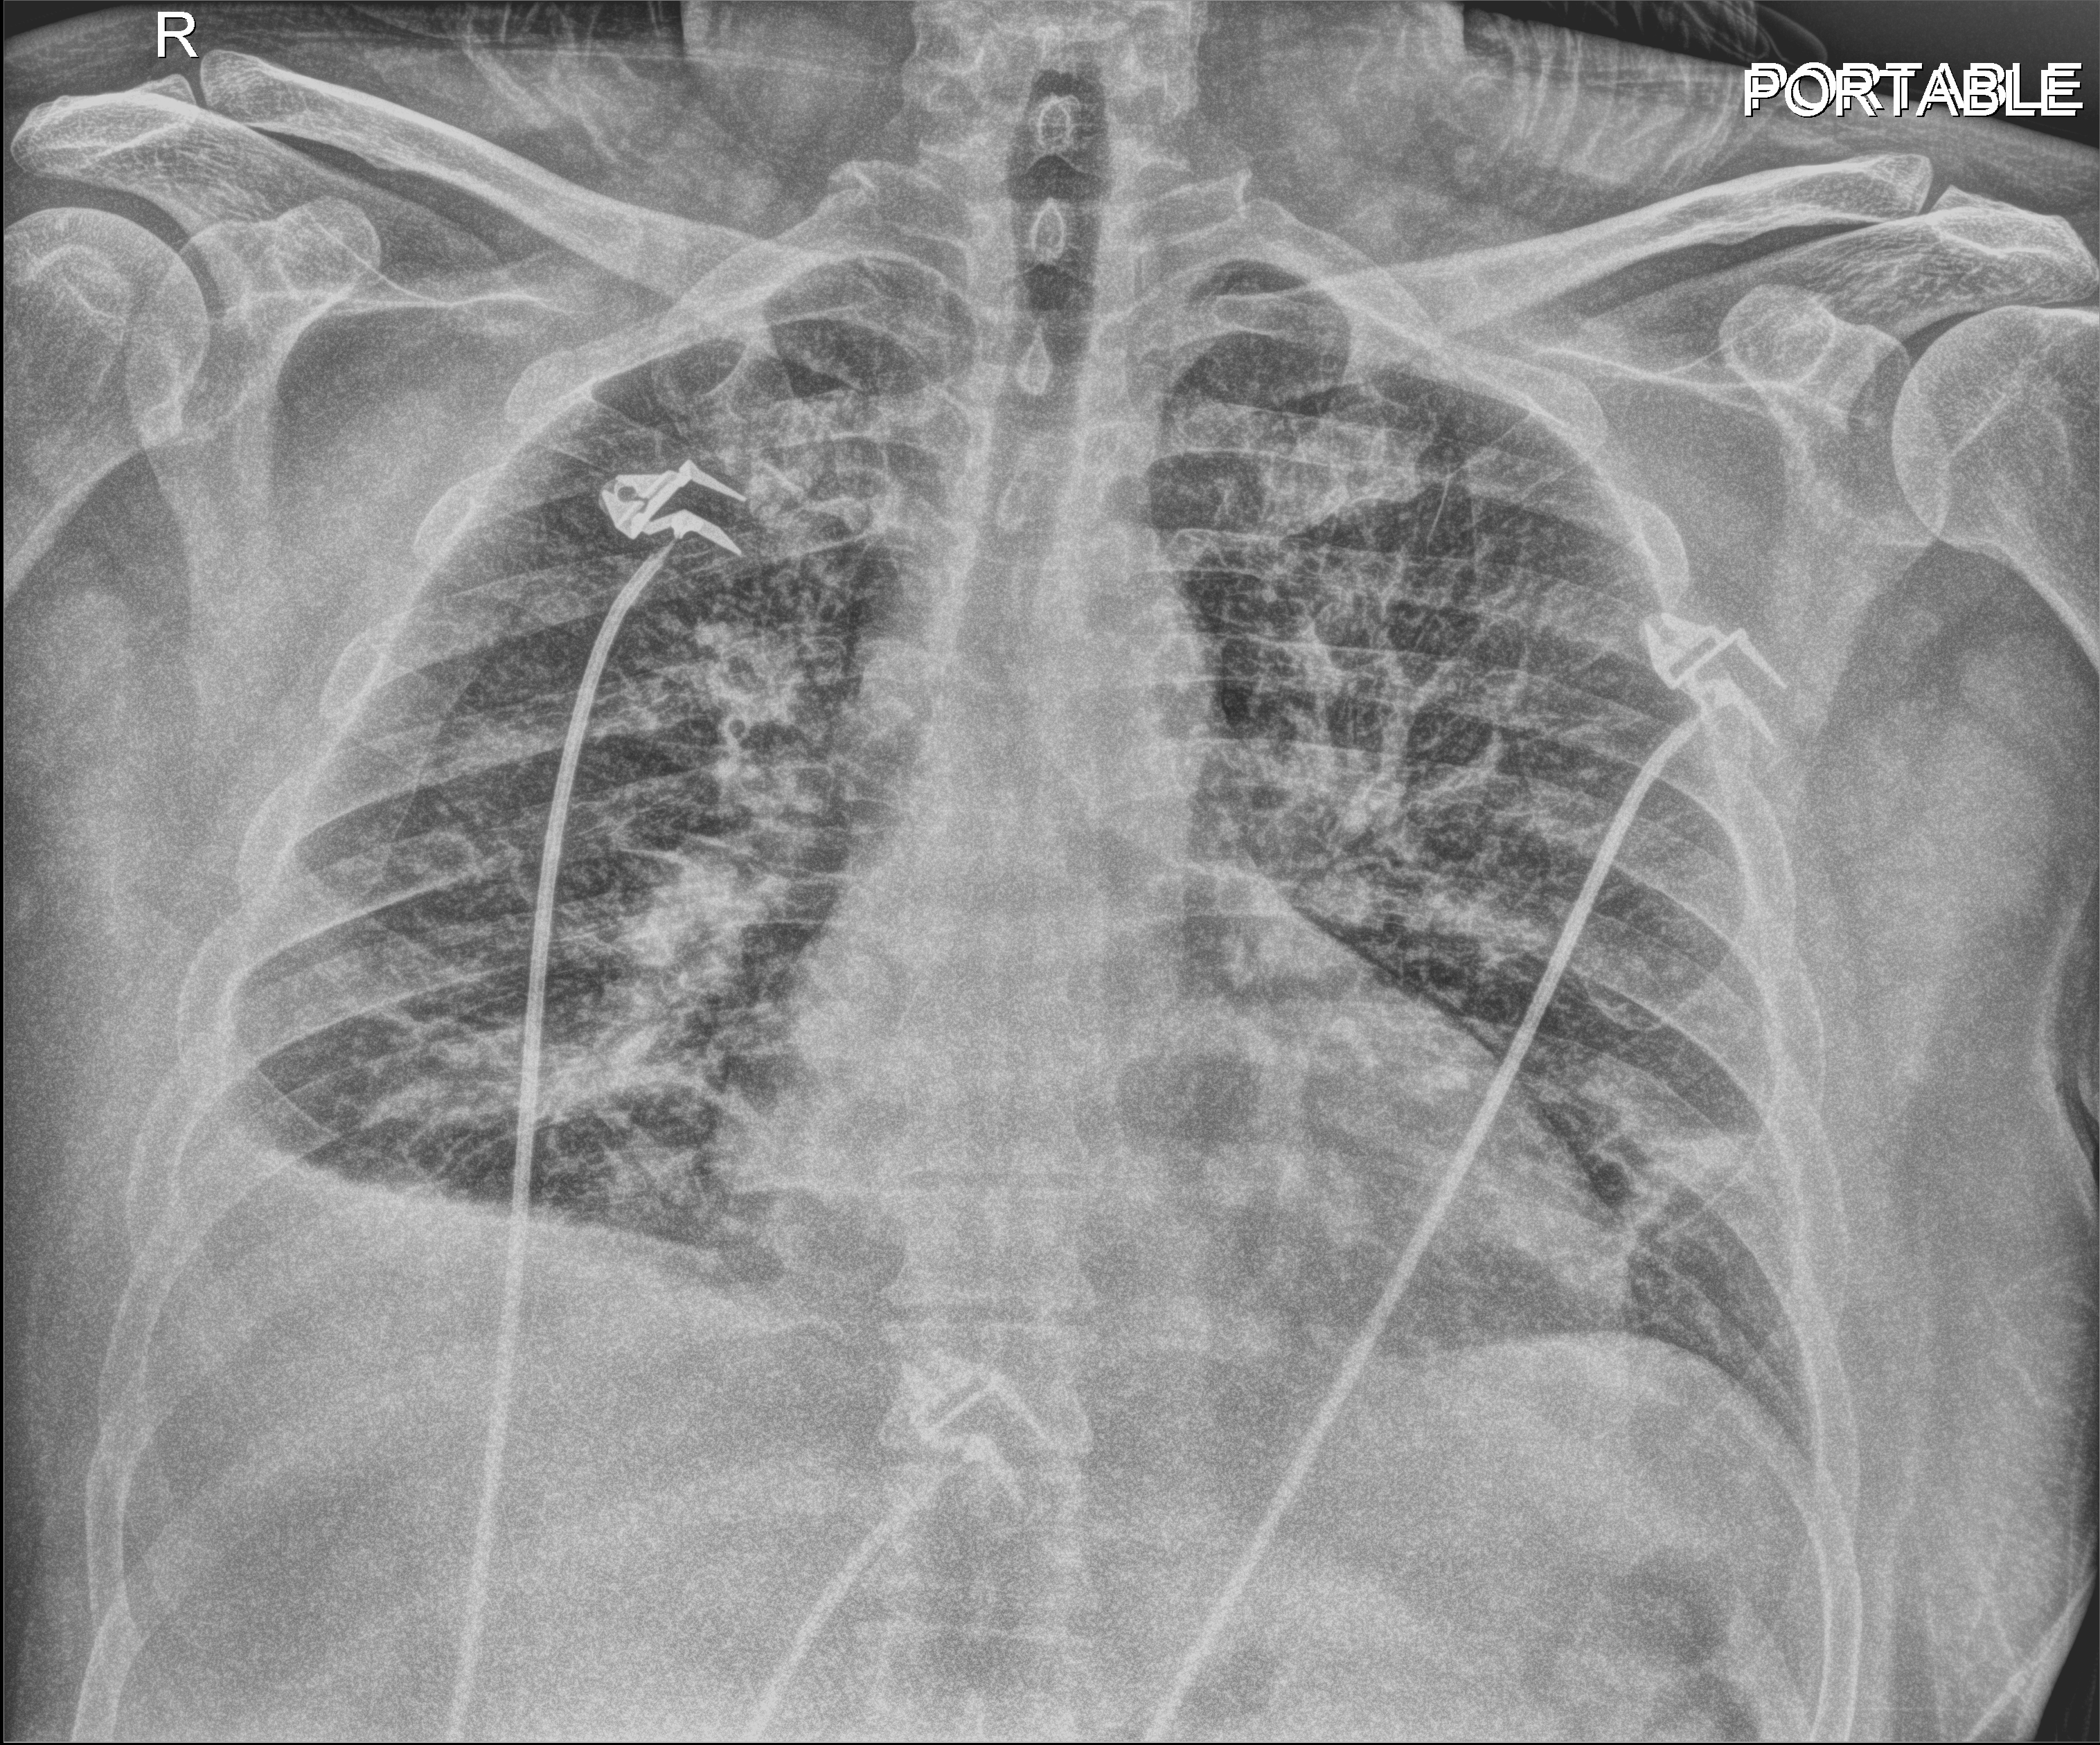
Portable chest radiograph. Patient hospitalised with COVID-19; male, aged 18–59 years.
From the hospital-stay record, not from the radiograph (when in the stay this image was taken is not recorded): length of hospital stay: 17 days; admitted to intensive care during this hospital stay: no.